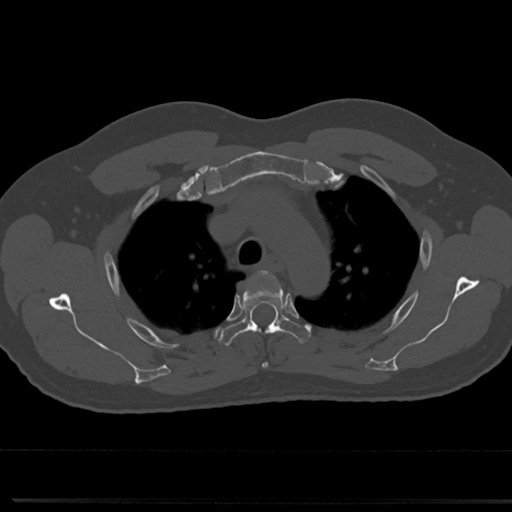
CT including the spine, one axial slice; reconstruction kernel Br40s/3; bone window (W 1800 / L 400 HU); 0.5 mm slice thickness; 512 × 512 image matrix. Male patient, age 61 years. Case-level facts recorded for this patient, not image findings: primary cancer: prostate.
Structures marked on this image (semi-automatically segmented with operator editing):
- T3 vertebra: bounding box (x1, y1, x2, y2) in pixels: (263, 271, 267, 367)
- T4 vertebra: (219, 271, 310, 345)